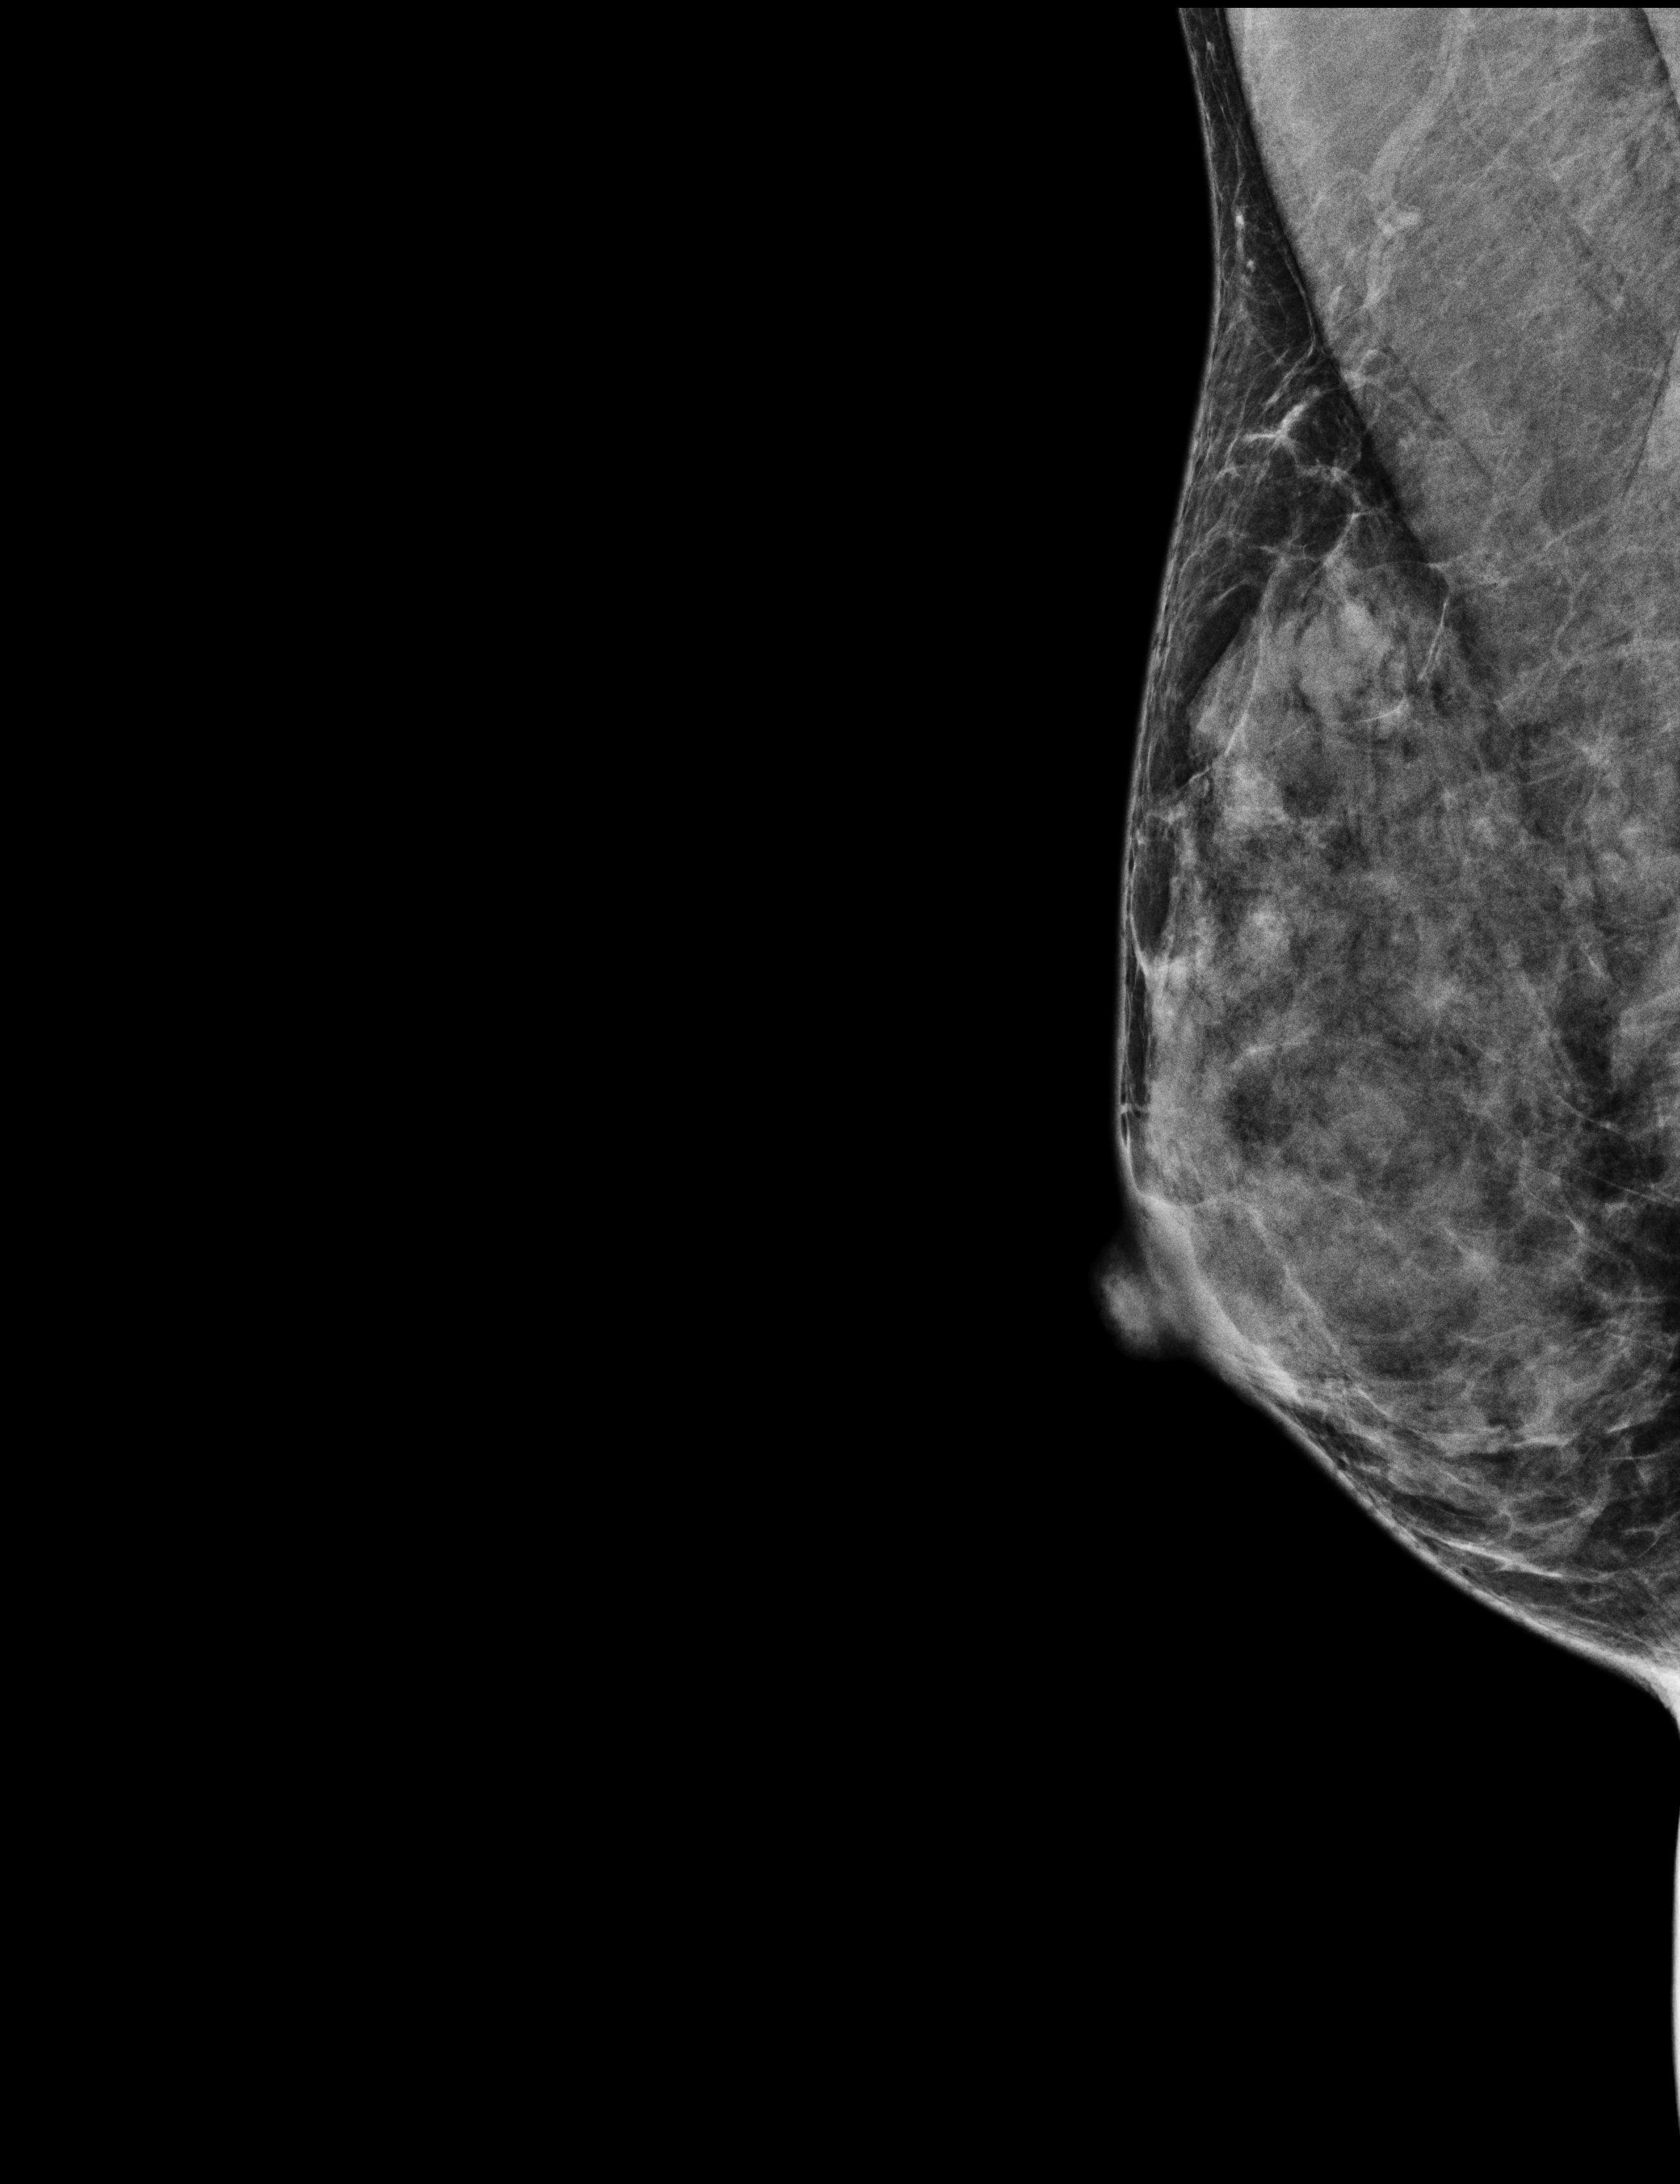
Screening examination, system: Selenia Dimensions. Patient aged 44 years (female).
Image type: full-field digital mammogram. Breast: right. Projection: mediolateral oblique (MLO) view.